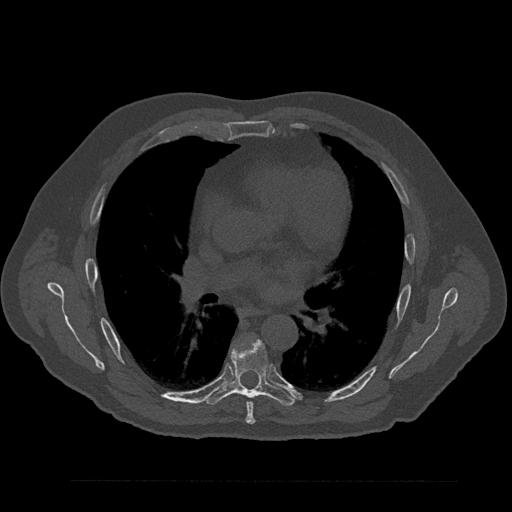
CT including the spine, one axial slice; reconstruction kernel Br40s/3; 120 kVp; bone window (W 1800 / L 400 HU); 512 × 512 image matrix. Patient: male, 61 years. Case-level facts recorded for this patient, not image findings: primary cancer: prostate.
Annotated regions visible in this slice (semi-automatically segmented with operator editing):
- T6 vertebra: bounding box <245,402,255,424> (left, top, right, bottom; pixels)
- T7 vertebra: <204,337,295,406>